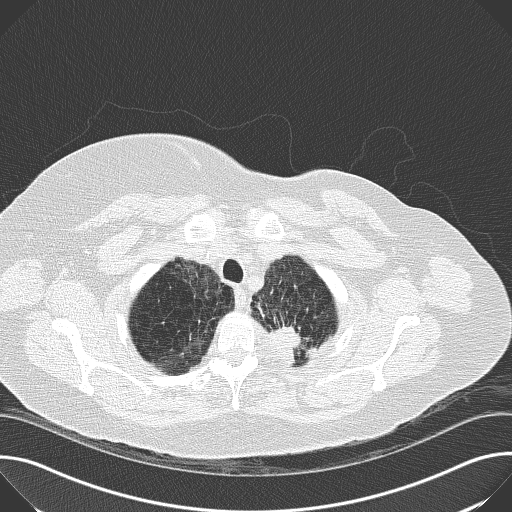
Low-dose screening chest CT, axial slice. Baseline annual screen. Lung window (W 1500 / L -600 HU). 2 mm slice thickness. Slice 149 of 169 in the series. 512 × 512 image matrix. Female, age 56 years at enrolment. Current smoker at enrolment.
• Expert-annotated lung lesion, box from (x=252, y=304) to (x=318, y=368) px.
• Reader record for this screening exam (exam-level; its link to the box is not recorded): non-calcified nodule or mass ≥4 mm, left upper lobe, 19 × 17 mm, spiculated (stellate) margins, soft tissue attenuation.
• Official screen result: positive, change unspecified: nodule(s) >= 4 mm or enlarging nodule(s), mass(es), or other non-specific abnormalities suspicious for lung cancer.